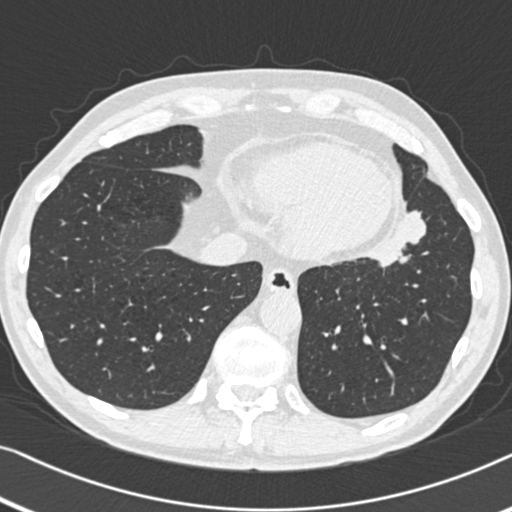
Low-dose screening chest CT, one axial slice; lung window (W 1500 / L -600 HU); 1 mm slice thickness; 512 × 512 image matrix, field of view 332 × 332 mm.
Annotated regions visible in this slice (manually delineated by an expert):
- lesion 1 (tumor, upper lobe of left lung): bounding box [x1, y1, x2, y2] px = [375, 210, 426, 268]